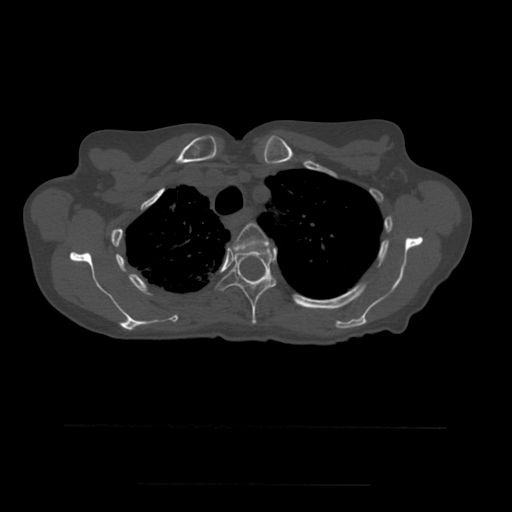
CT including the spine, one axial slice; slice 410 of 544 in the series (ordered by position); bone window (W 1800 / L 400 HU); 1.25 mm slice thickness; 512 × 512 image matrix, field of view 350 × 350 mm. Patient age 58 years. From the clinical record (not read from this slice): primary cancer: lung.
Annotated regions visible in this slice (semi-automatic segmentation, software-assisted and operator-edited):
- T3 vertebra: box from (x=233, y=223) to (x=270, y=254) px
- T4 vertebra: (x=216, y=248)–(x=276, y=324)